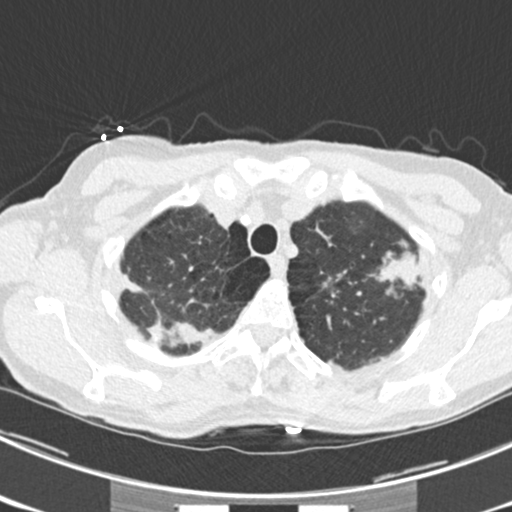
Low-dose screening chest CT, one axial slice. Reconstruction kernel B30f. Lung window (W 1500 / L -600 HU). 2 mm slice thickness. 512 × 512 image matrix, field of view 302 × 302 mm.
Outlined on this slice (expert manual segmentation):
- lesion 1 (tumor, upper lobe of left lung): box from (x=378, y=255) to (x=419, y=286) px
- lesion 4 (tumor, upper lobe of right lung): (x=151, y=322)–(x=201, y=345)